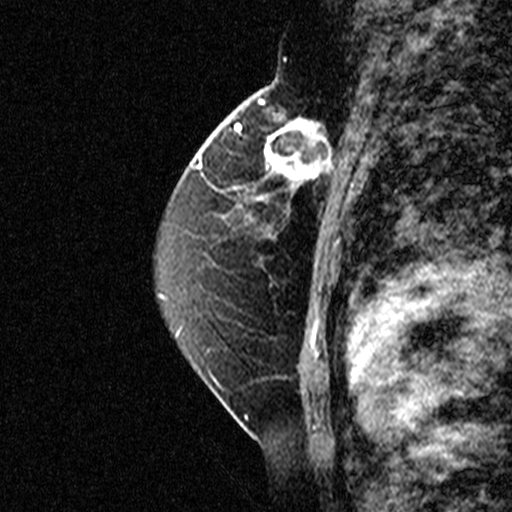
Breast MRI (dynamic contrast-enhanced), one sagittal slice; dynamic contrast-enhanced study with each time point stored as its own series, time point 2 of 3 at this slice position (early post-contrast, ordered by acquisition time); 1.5 T; TE 4.5 ms, TR 11 ms; 3 mm slice thickness; 512 × 512 image matrix, field of view 200 × 200 mm. Female patient, age 49 years. From the clinical record (not read from this slice): setting: breast cancer imaged before/during neoadjuvant chemotherapy; receptor status: triple-negative.
Outlined on this slice (semi-automatic segmentation, software-assisted and operator-edited):
- analysis volume of interest (the breast-tissue region the enhancement analysis was run in; not a lesion): bounding box <254,112,347,207> (left, top, right, bottom; pixels)
- tumour enhancement mask (voxels above the 90 % enhancement threshold inside the analysis volume of interest): <254,112,347,207>